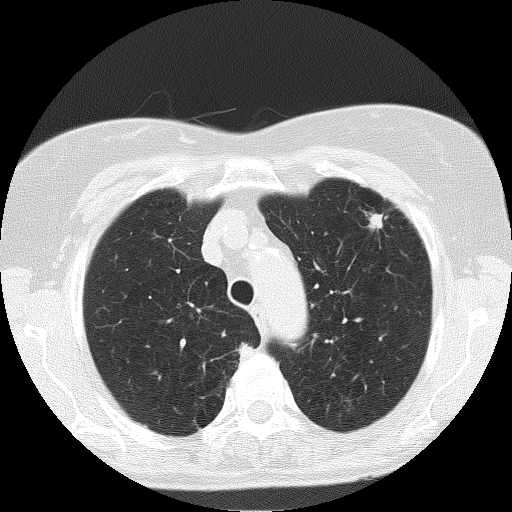
Low-dose screening chest CT, one axial slice; slice 134 of 166 in the series (ordered by position); 120 kVp; lung window (W 1500 / L -600 HU); 2 mm slice thickness; 512 × 512 image matrix, field of view 303 × 303 mm.
Structures marked on this image (manually delineated by an expert):
- lesion 1 (tumor, upper lobe of left lung): bounding box <370,213,384,229> (left, top, right, bottom; pixels)